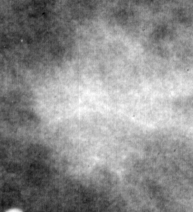
Crop from a digitized film mammogram around one marked abnormality; right breast; MLO view; BI-RADS breast density category 3 (scale 1–4).
Mass, shape lobulated, margins ill defined; BI-RADS assessment category 4; subtlety rating 4 on a 1 (subtle) to 5 (obvious) scale; pathology (as recorded): malignant.